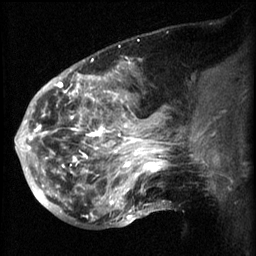
Breast MRI (dynamic contrast-enhanced), one sagittal slice; position 25 of 60 along the scan axis; 3 images stored at this slice position (order not interpretable as contrast timing); 1.5 T; TE 4.2 ms, TR 8.2 ms; 2.3 mm slice thickness; 256 × 256 image matrix, field of view 200 × 200 mm. Female patient, age 50 years.
Annotated regions visible in this slice (semi-automatic segmentation, software-assisted and operator-edited):
- analysis volume of interest (the breast-tissue region the enhancement analysis was run in; not a lesion): bounding box [x1, y1, x2, y2] px = [50, 64, 169, 217]
- tumour enhancement mask (voxels above the 70 % enhancement threshold inside the analysis volume of interest): [50, 66, 169, 217]